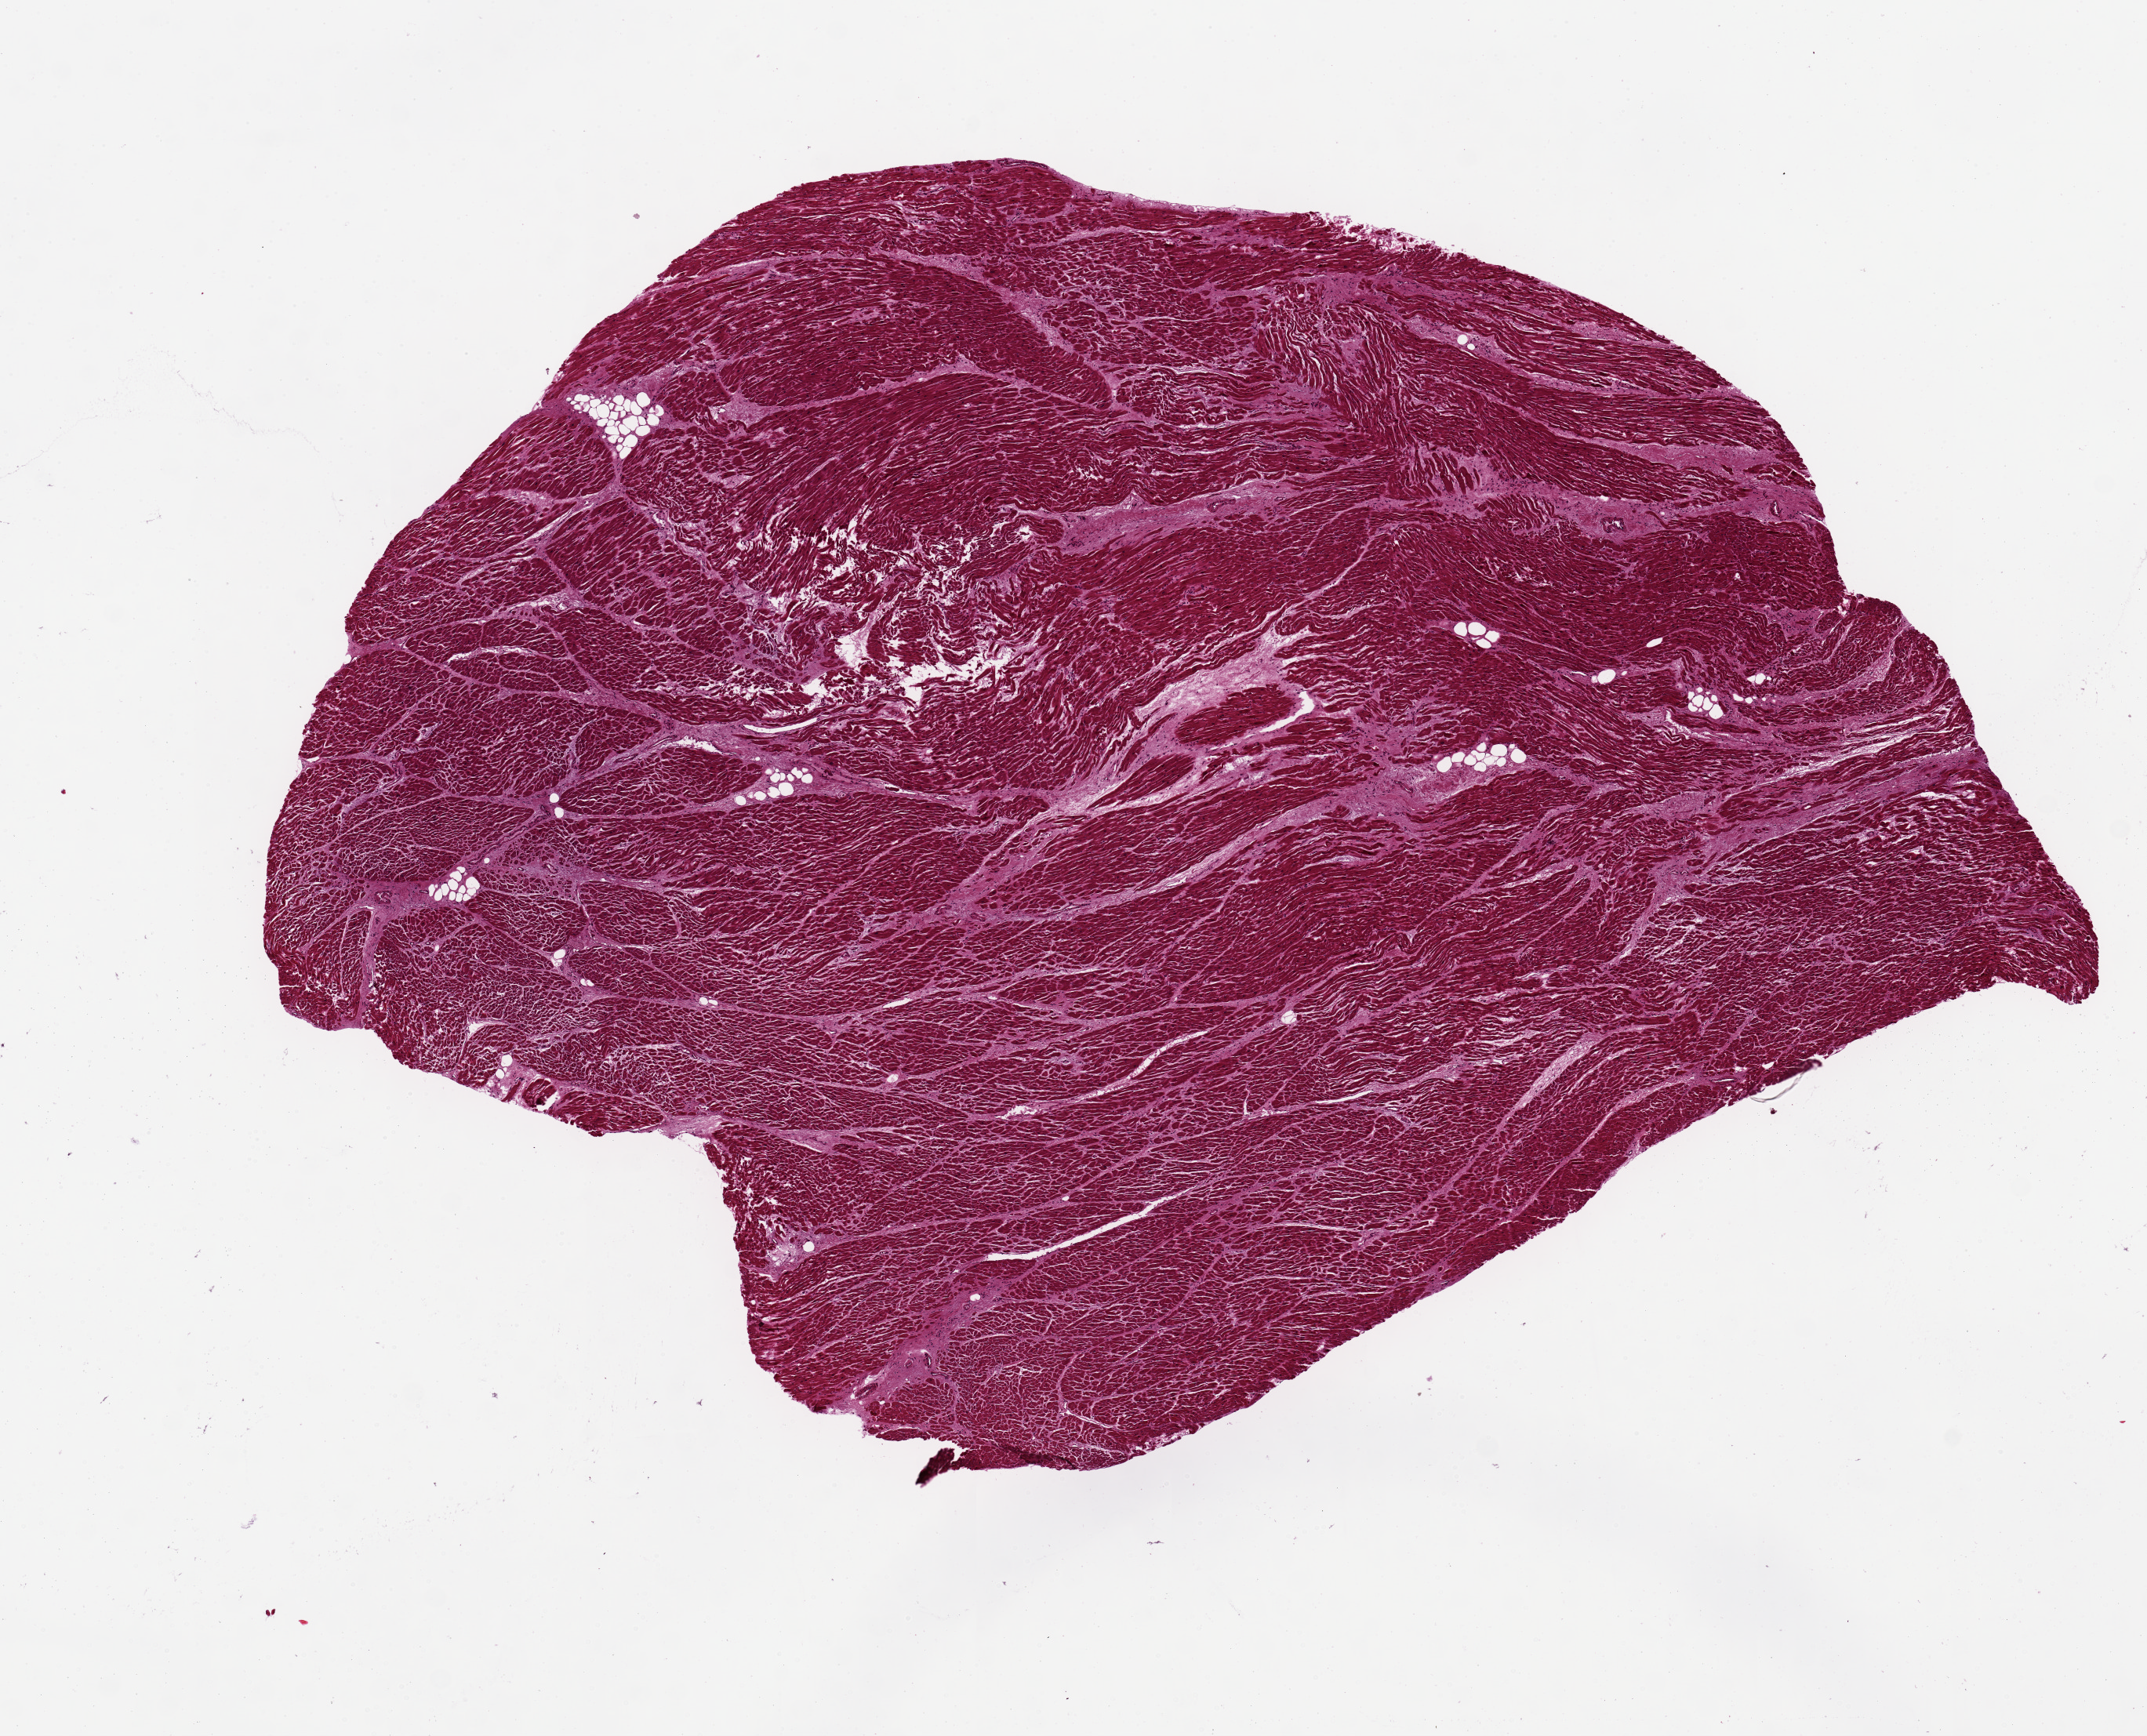
Whole-slide image, hematoxylin and eosin (H&E) stain, brightfield, a low-resolution overview of the entire scanned area, about 10.8 x 8.8 mm, PAXgene-fixed paraffin-embedded (PFPE) section, sampled site (target tissue): heart, donor tissue sample.
Review note (as recorded): 7.5x6mm aliquot.